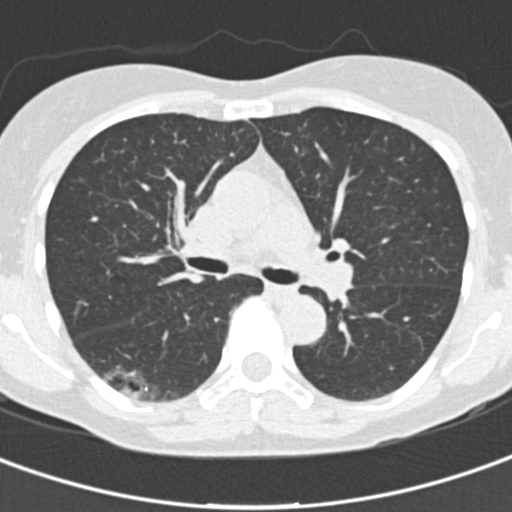
Low-dose screening chest CT, axial slice. Baseline annual screen. Lung window (W 1500 / L -600 HU). Slice 68 of 162 in the series. Female participant, aged 64 years at enrolment. Current smoker at enrolment.
Expert-annotated lung lesion, bounding box <82,348,174,414> (left, top, right, bottom; pixels). The exam's reader record, not a measurement of the box and not confirmed to be the same lesion: non-calcified nodule or mass ≥4 mm, right lower lobe, 31 × 15 mm, poorly defined margins, ground glass attenuation. Official screen result: positive, change unspecified: nodule(s) >= 4 mm or enlarging nodule(s), mass(es), or other non-specific abnormalities suspicious for lung cancer. Participant outcome: lung cancer diagnosed 91 days after this screen — bronchiolo-alveolar carcinoma, non-mucinous, right lower lobe, well differentiated (G1), stage IA (AJCC 6th edition), 20 mm at pathology.